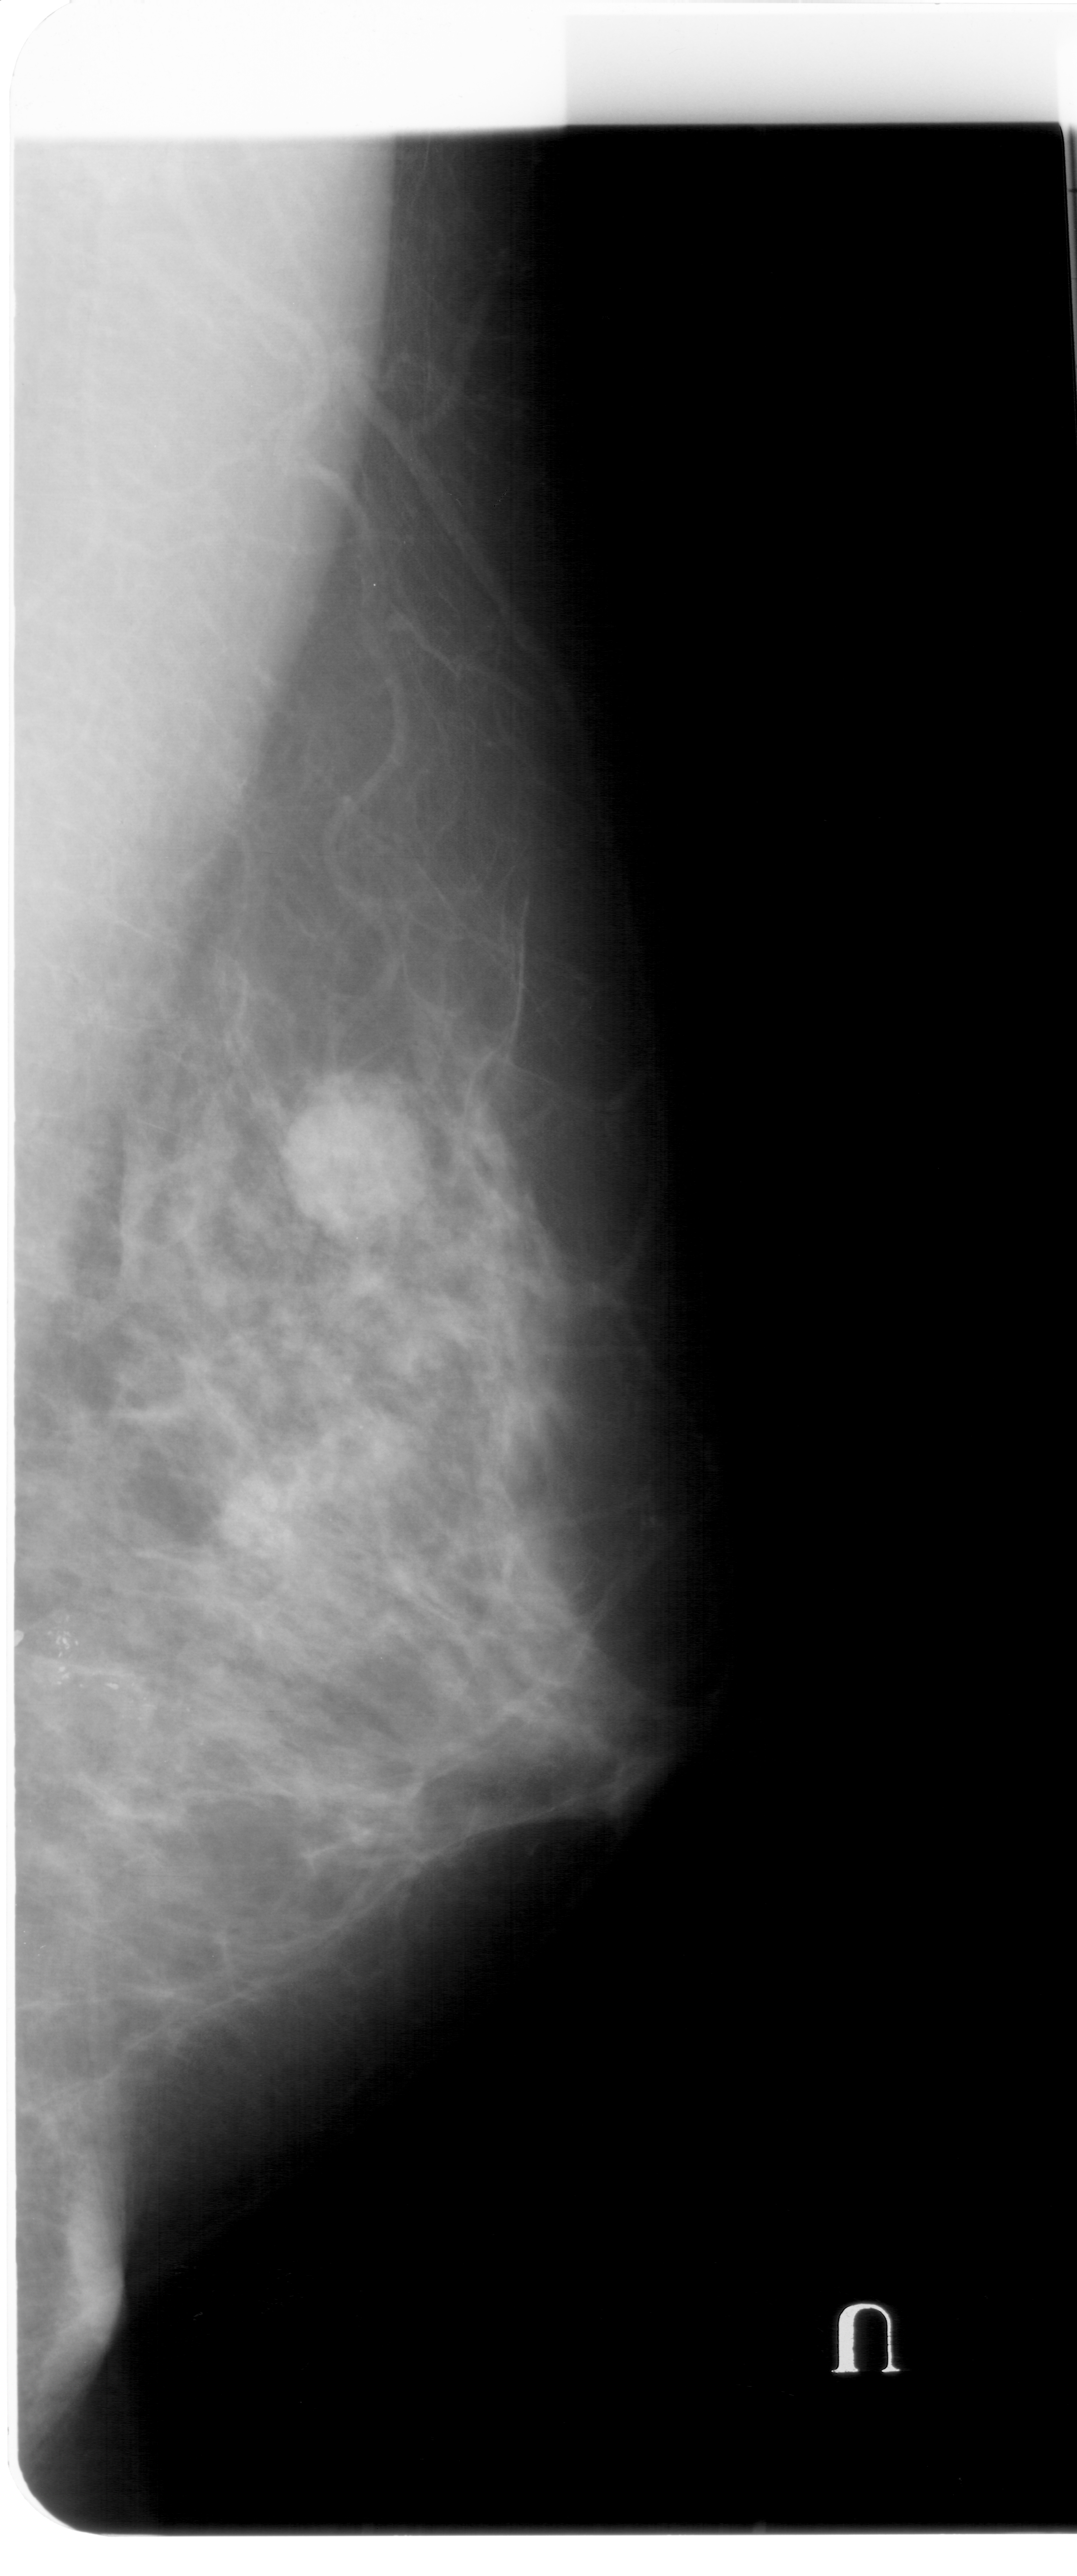
Scanned film-screen mammogram. Right breast. Mediolateral oblique (MLO) view. BI-RADS breast density category 3 (scale 1–4). 1077 × 2576 image matrix.
Marked abnormalities (boxes around the expert regions of interest):
- calcifications, morphology pleomorphic, distribution clustered; BI-RADS assessment category 4; subtlety rating 3 on a 1 (subtle) to 5 (obvious) scale; pathology result (as recorded, not read from the image): malignant: box from (x=31, y=1611) to (x=232, y=1774) px